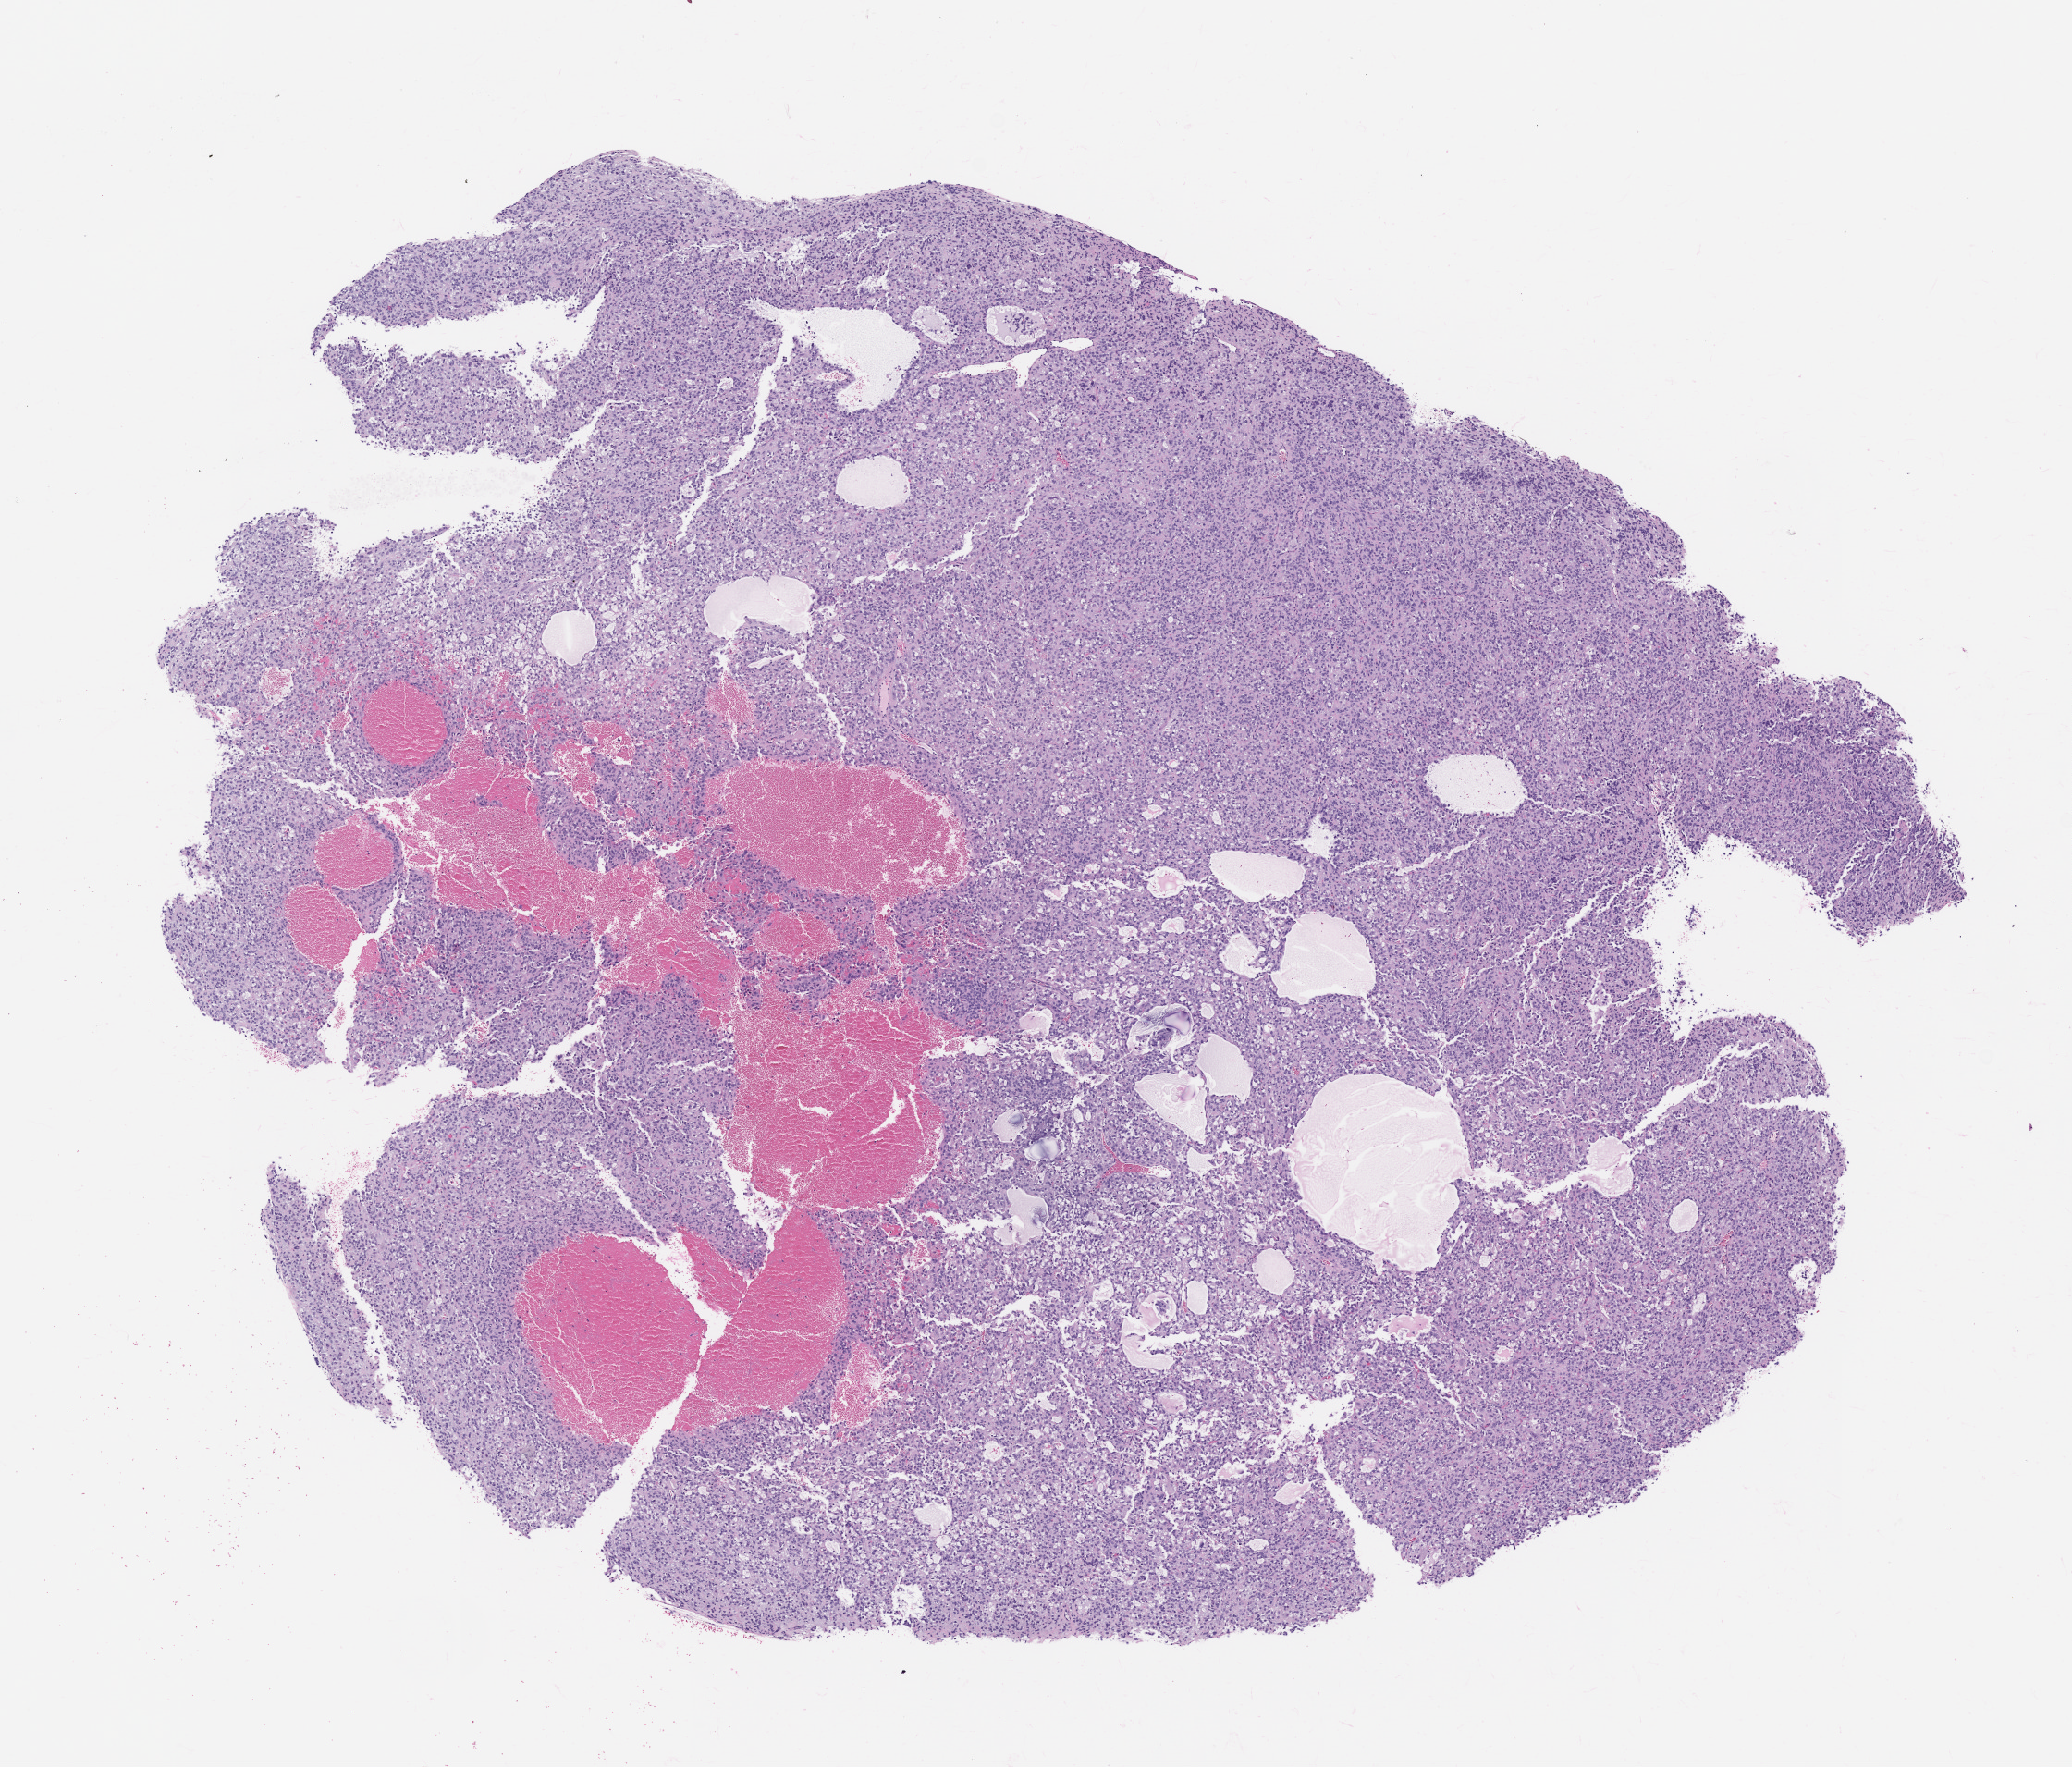
Whole-slide image, haematoxylin and eosin: patient-derived xenograft (human tumor grown in a mouse), passage 1 — shown as a low-resolution overview of the whole scanned area (about 9.0 x 7.7 mm). FFPE section. Tumor site category: uterus.
Originating patient diagnosis: Leiomyosarcoma.